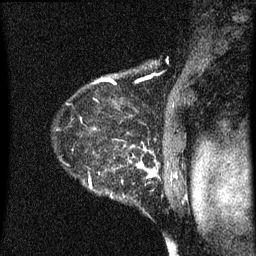
Breast MRI (dynamic contrast-enhanced), one sagittal slice. Position 53 of 60 along the scan axis. Dynamic contrast-enhanced series, image 2 of 3 at this slice position (ordered by acquisition). 1.5 T. TE 4.2 ms, TR 8 ms. 2 mm slice thickness. 256 × 256 image matrix, field of view 180 × 180 mm. Female patient, age 54 years.
Annotated regions visible in this slice (semi-automatic segmentation, software-assisted and operator-edited):
- analysis volume of interest (the breast-tissue region the enhancement analysis was run in; not a lesion): bounding box [x1, y1, x2, y2] px = [55, 140, 164, 209]
- tumour enhancement mask (voxels above the 70 % enhancement threshold inside the analysis volume of interest): [73, 146, 159, 197]